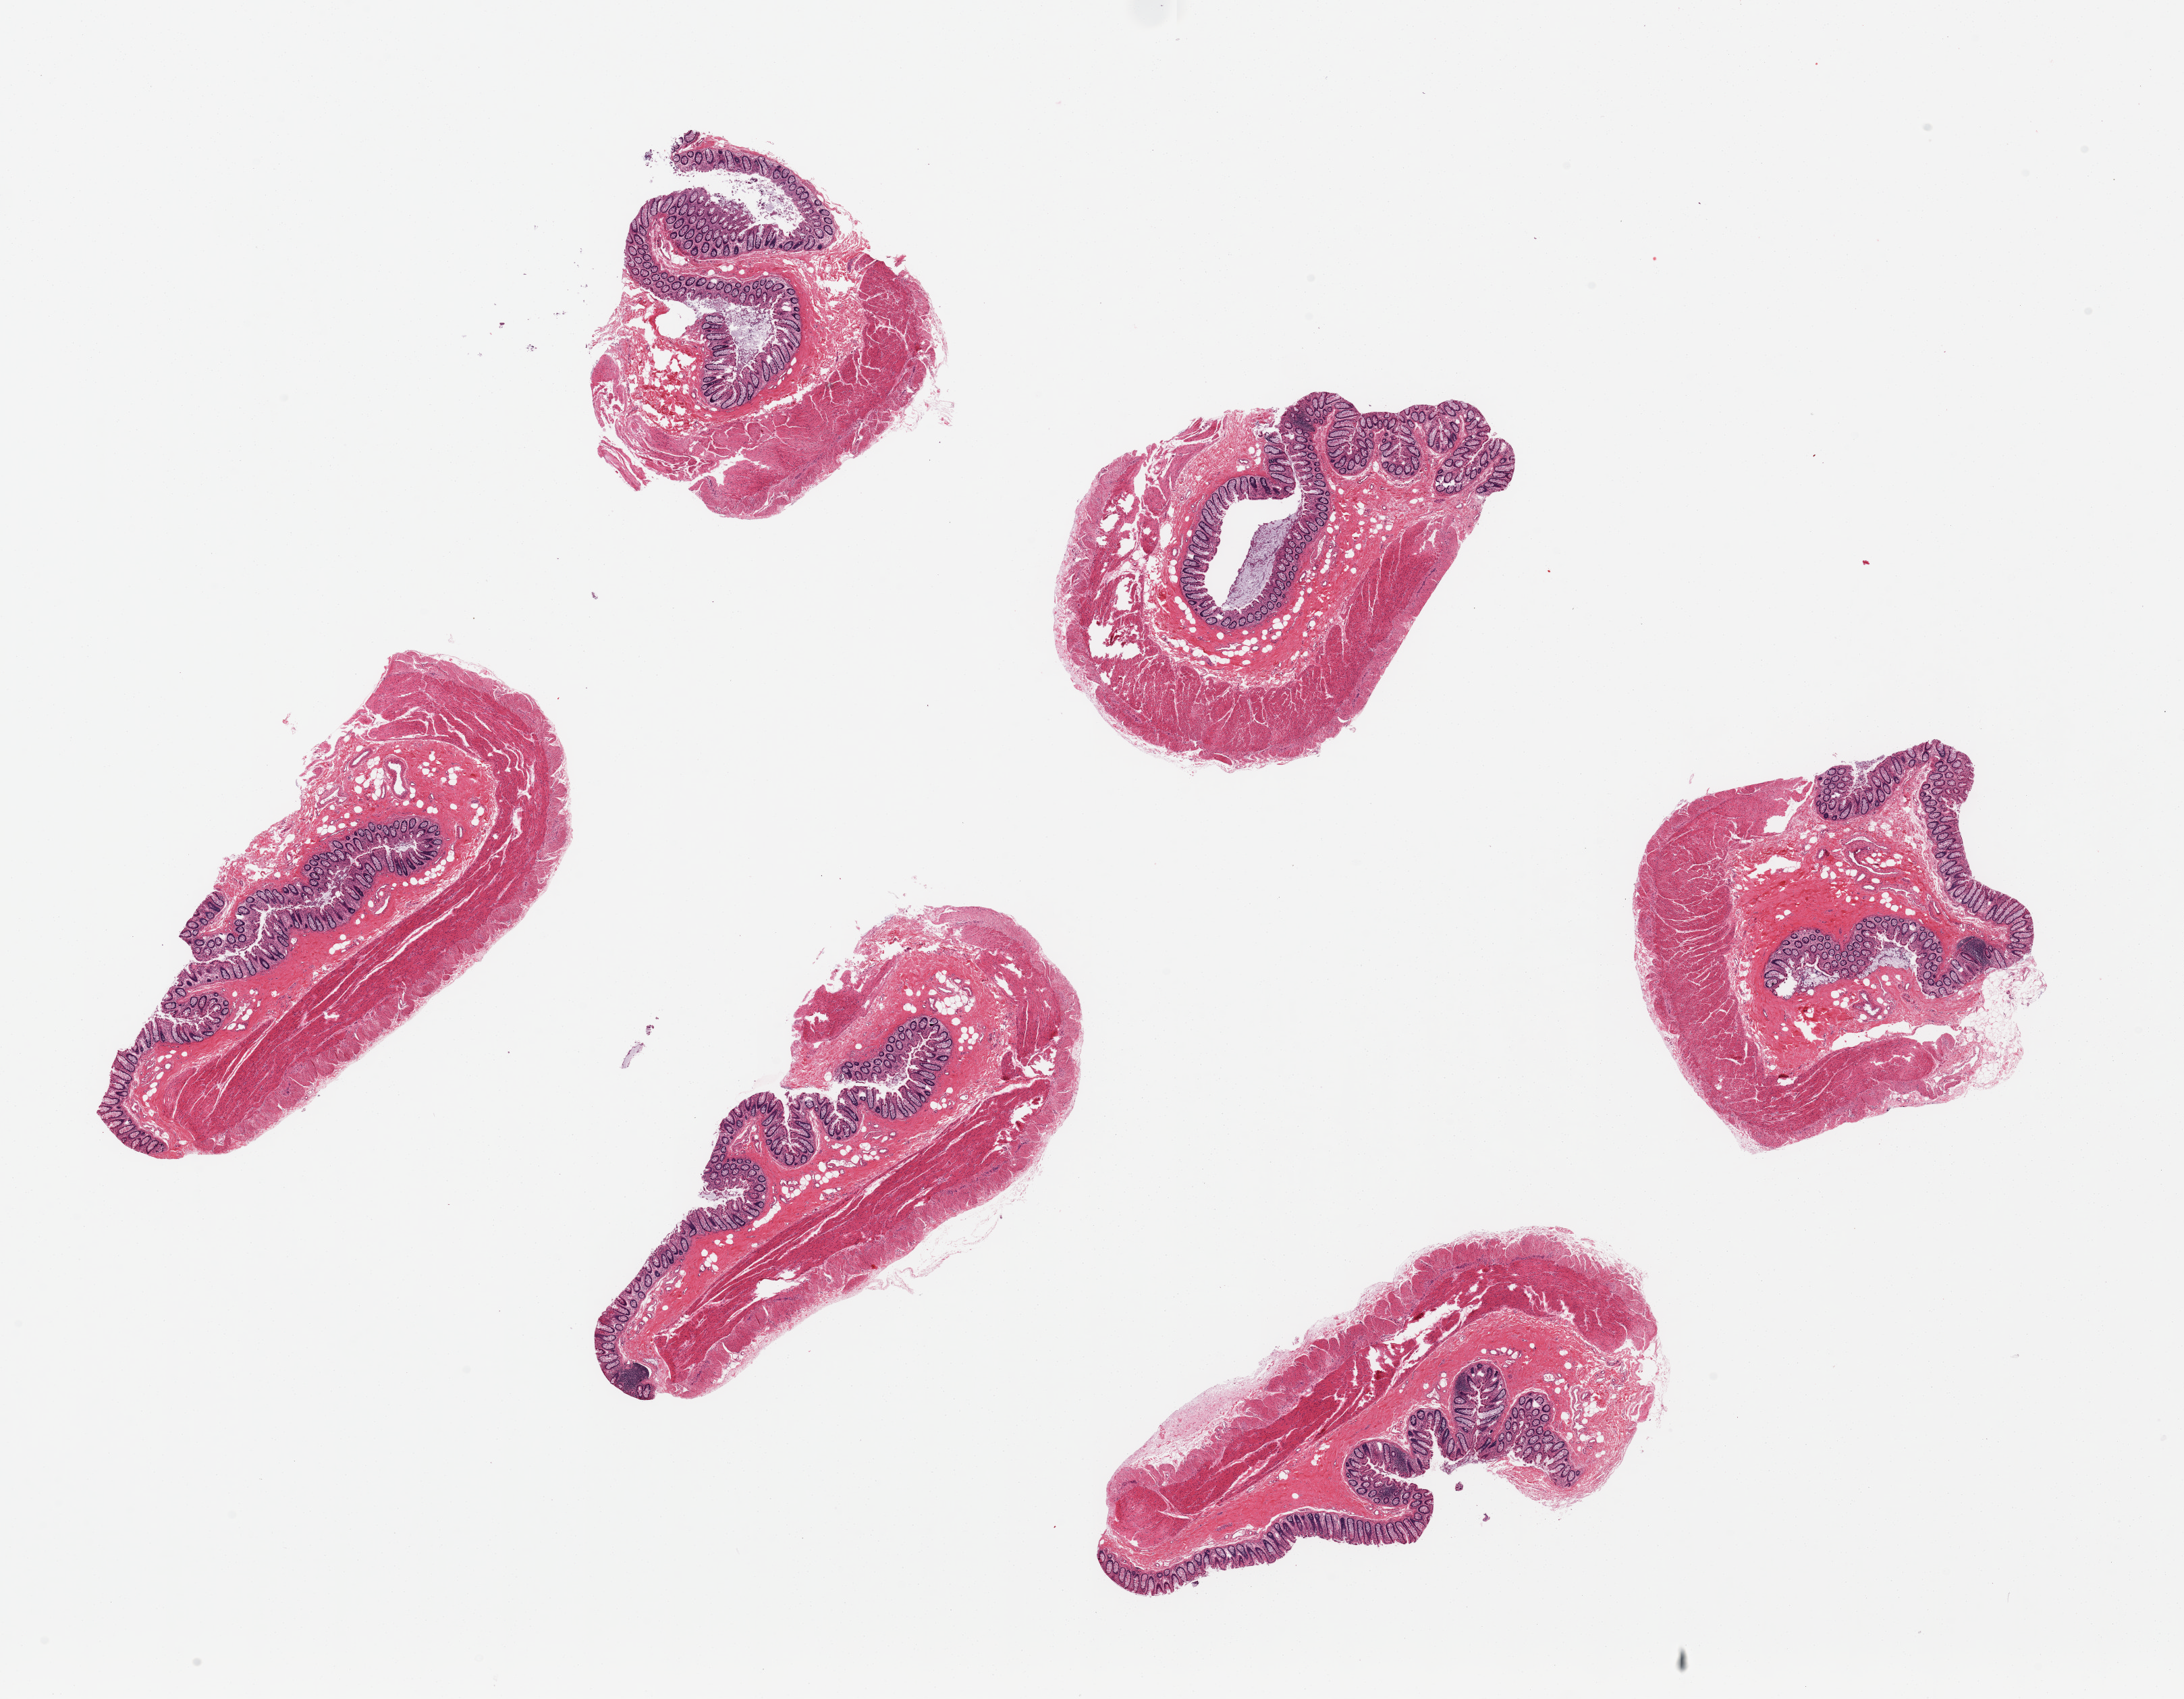
H&E whole-slide image — a low-resolution overview of the entire scanned area, about 25.6 x 19.9 mm; PAXgene-fixed paraffin-embedded (PFPE) section; target tissue: transverse colon; donor tissue sample. Male donor.
* reviewer comment on this tissue sample: 6 pieces ~7x2mm. Mucosa is ~10% thickness, fairly well-preserved